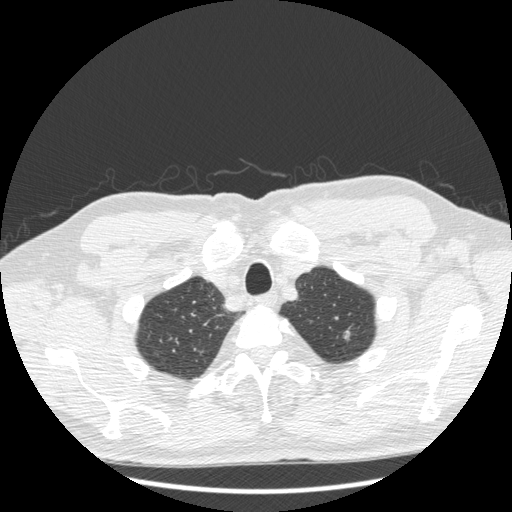
Chest CT (low-dose screening protocol), one axial image, third annual screen, lung window (W 1500 / L -600 HU), 1.25 mm slice thickness, standard (soft-tissue) reconstruction kernel (STANDARD), slice 31 of 223 in the series. Male participant, aged 69 years at enrolment. Former smoker at enrolment.
- Lesion marked by an expert reader, bounding box (x1, y1, x2, y2) in pixels: (329, 319, 362, 345).
- Reader record for this screening exam (exam-level; its link to the box is not recorded): non-calcified nodule or mass ≥4 mm, left upper lobe, 7 × 6 mm, smooth margins, soft tissue attenuation, pre-existing on the prior screen: yes; interval growth: yes.
- Official screen result: positive, other.
- Later outcome: lung cancer diagnosed 112 days after this screen — adenocarcinoma, NOS, left upper lobe, moderately differentiated (G2), stage IA (AJCC 6th edition), 10 mm at pathology.